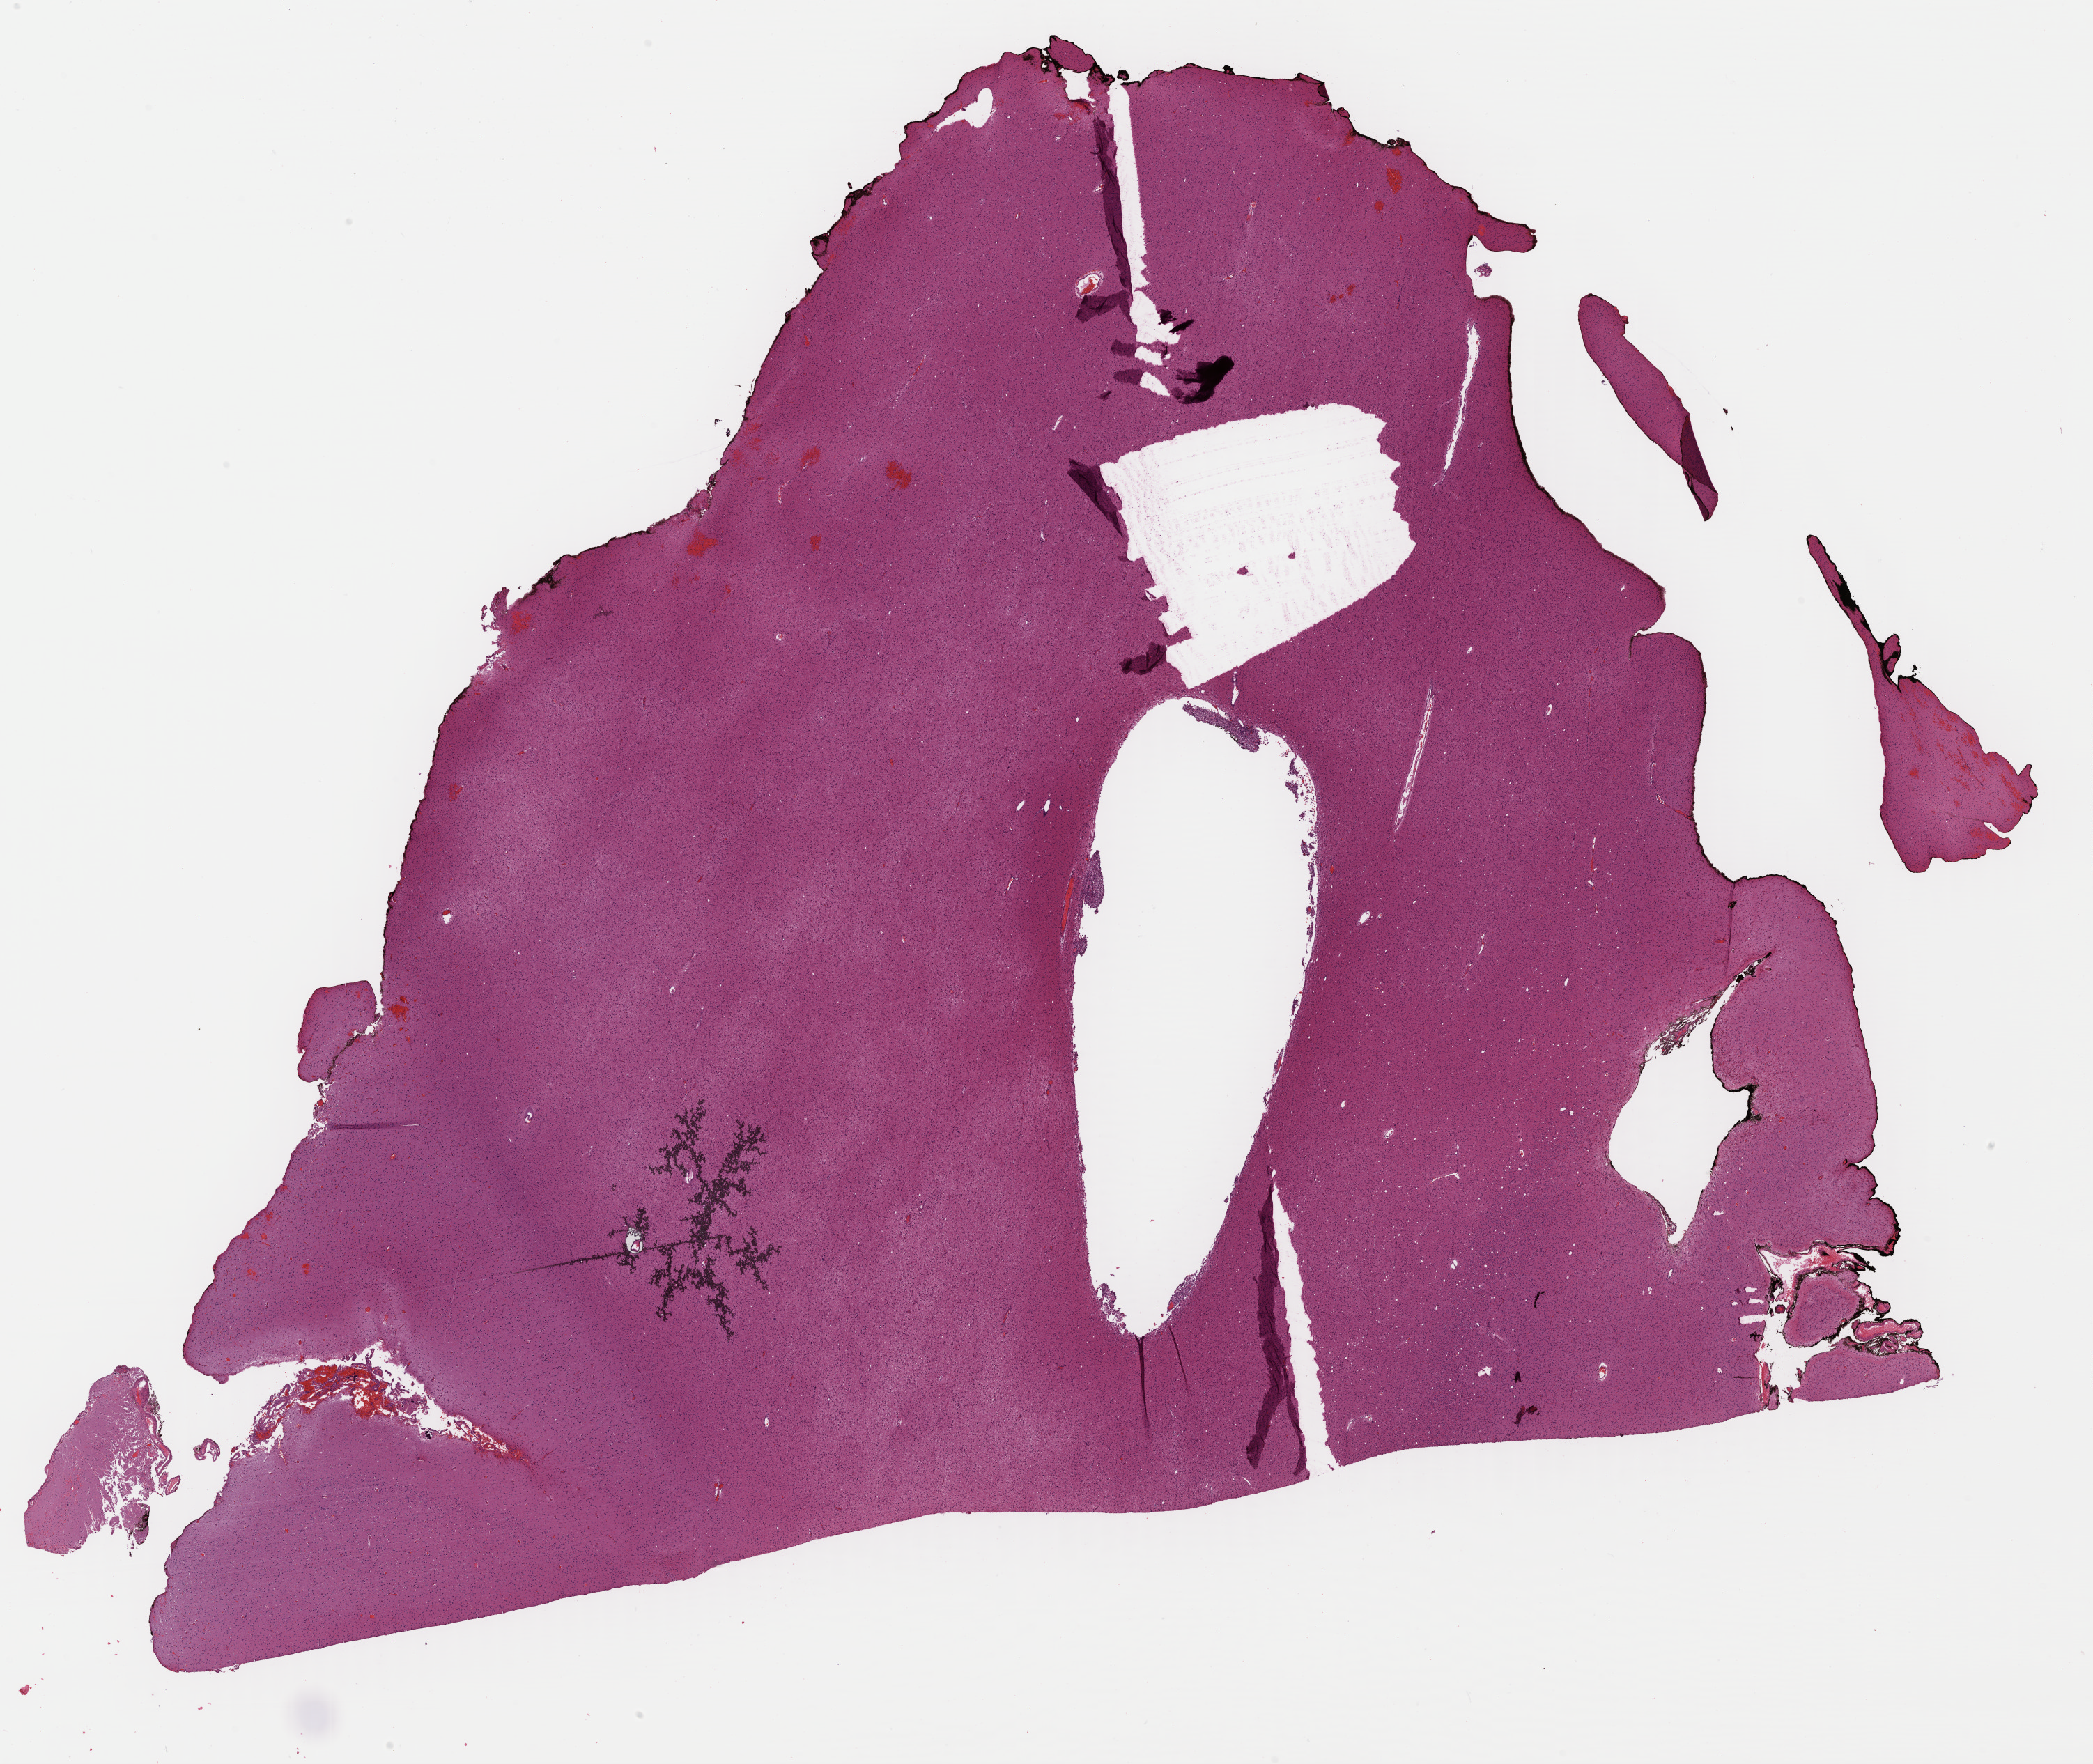
Digitized Hematoxylin and eosin (H&E) stained tissue section (whole slide), low-resolution overview of the scanned area, about 23.6 x 19.9 mm (from a 40x scan). Formalin-fixed paraffin-embedded (FFPE) diagnostic section. Primary tumour sample from the brain. Female patient; age at initial diagnosis 61 years. Histologic grade: G2 (moderately differentiated).
• diagnosis: Astrocytoma, NOS (cerebrum)